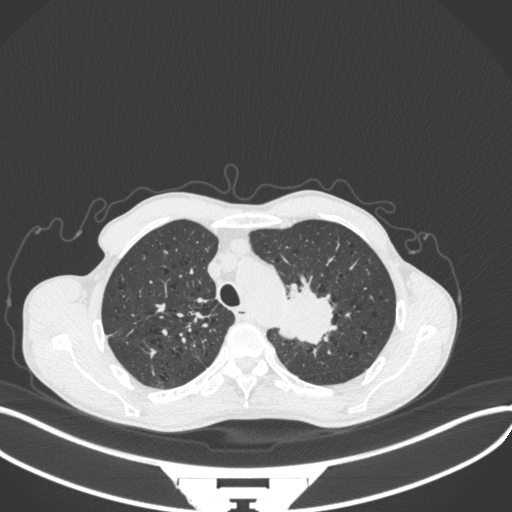
Chest CT, one axial slice; slice 330 of 394 in the series (ordered by position); 120 kVp; lung window (W 1500 / L -600 HU); 1 mm slice thickness; 512 × 512 image matrix, field of view 400 × 400 mm. Male patient, age 65 years. From the clinical record (not read from this slice): clinical TNM (as recorded): T2b N0 M0; histopathological grade: G2.
Annotated regions visible in this slice (bounding box drawn by a radiologist):
- lung tumour (recorded histology: adenocarcinoma): box from (x=276, y=273) to (x=340, y=348) px